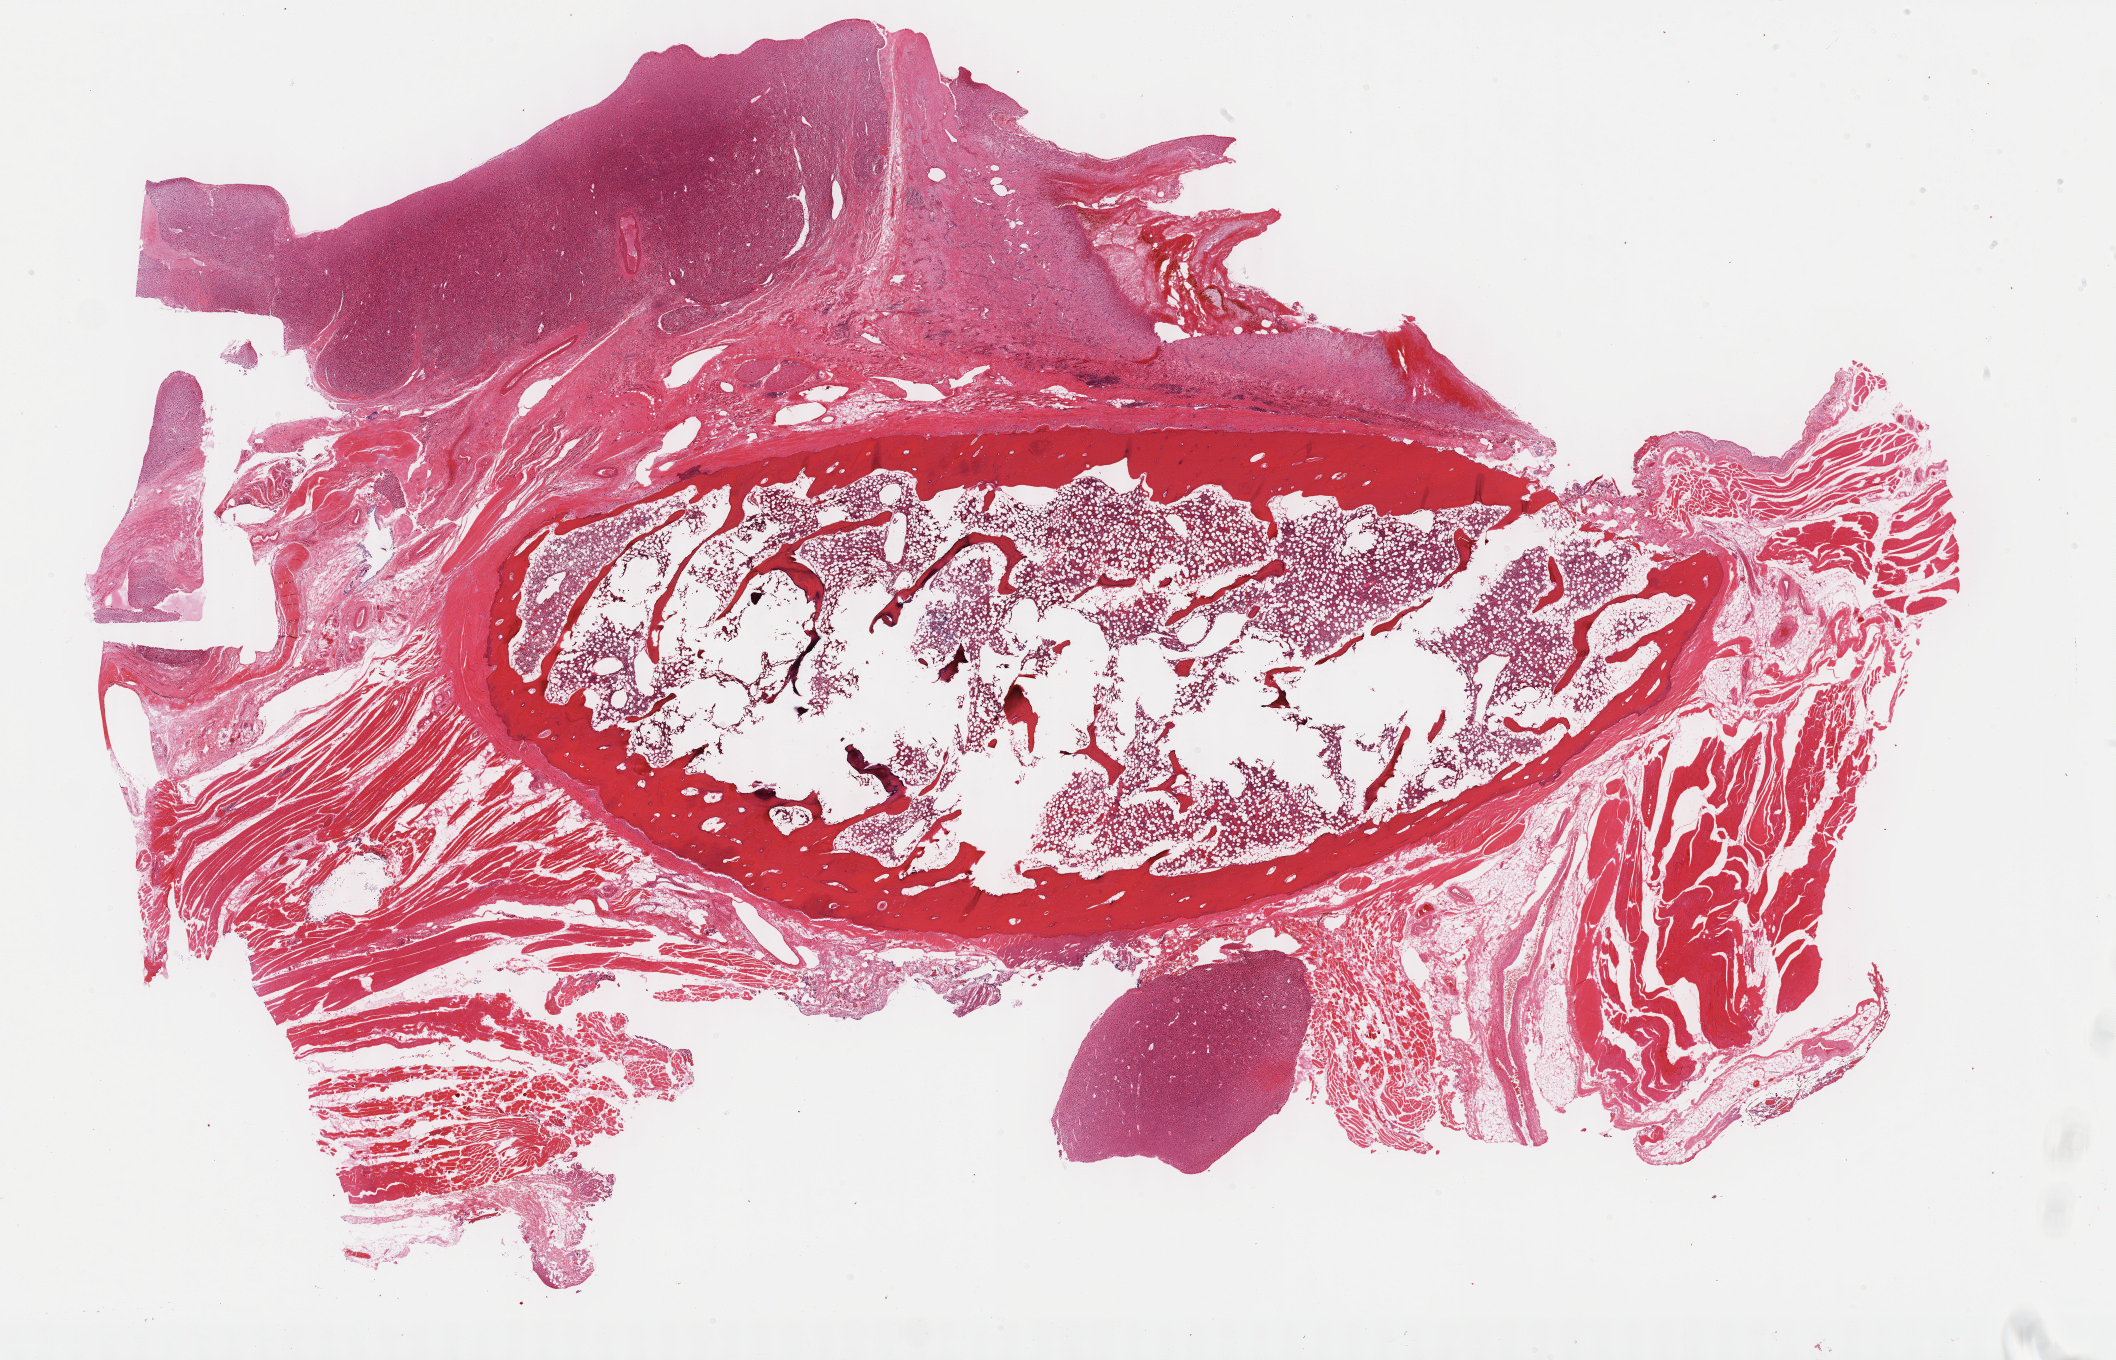
H&E whole-slide image, low-resolution overview of the scanned area, about 34.2 x 22.0 mm (from a 40x scan). Formalin-fixed paraffin-embedded (FFPE) diagnostic section. Sample: primary tumour, connective, subcutaneous and other soft tissues. Female patient; age at initial diagnosis 49 years.
Histologic diagnosis: Undifferentiated sarcoma.